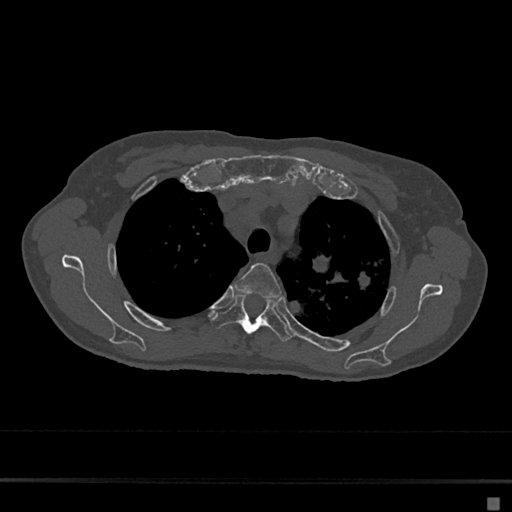
CT including the spine, one axial slice. Position 516 of 797 along the scan axis. 120 kVp. Bone window (W 1800 / L 400 HU). 0.5 mm slice thickness. 512 × 512 image matrix, field of view 360 × 360 mm. Patient: female, 68 years. From the clinical record (not read from this slice): primary cancer: renal.
Annotated regions visible in this slice (semi-automatically segmented with operator editing):
- T3 vertebra: bounding box [x1, y1, x2, y2] px = [234, 263, 281, 299]
- T4 vertebra: [210, 296, 291, 342]